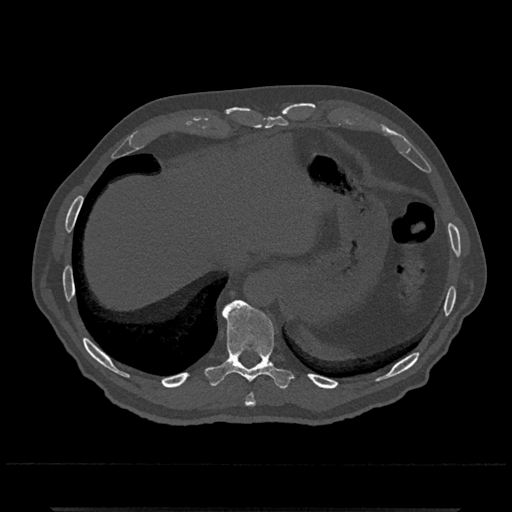
CT including the spine, one axial slice. Slice 556 of 797 in the series (ordered by position). Bone window (W 1800 / L 400 HU). 0.5 mm slice thickness. 512 × 512 image matrix, field of view 393 × 393 mm. Male patient, age 67 years. Case-level facts recorded for this patient, not image findings: primary cancer: prostate.
Annotated regions visible in this slice (semi-automatic segmentation, software-assisted and operator-edited):
- T10 vertebra: bounding box [x1, y1, x2, y2] px = [204, 299, 293, 389]
- T9 vertebra: [245, 394, 256, 407]